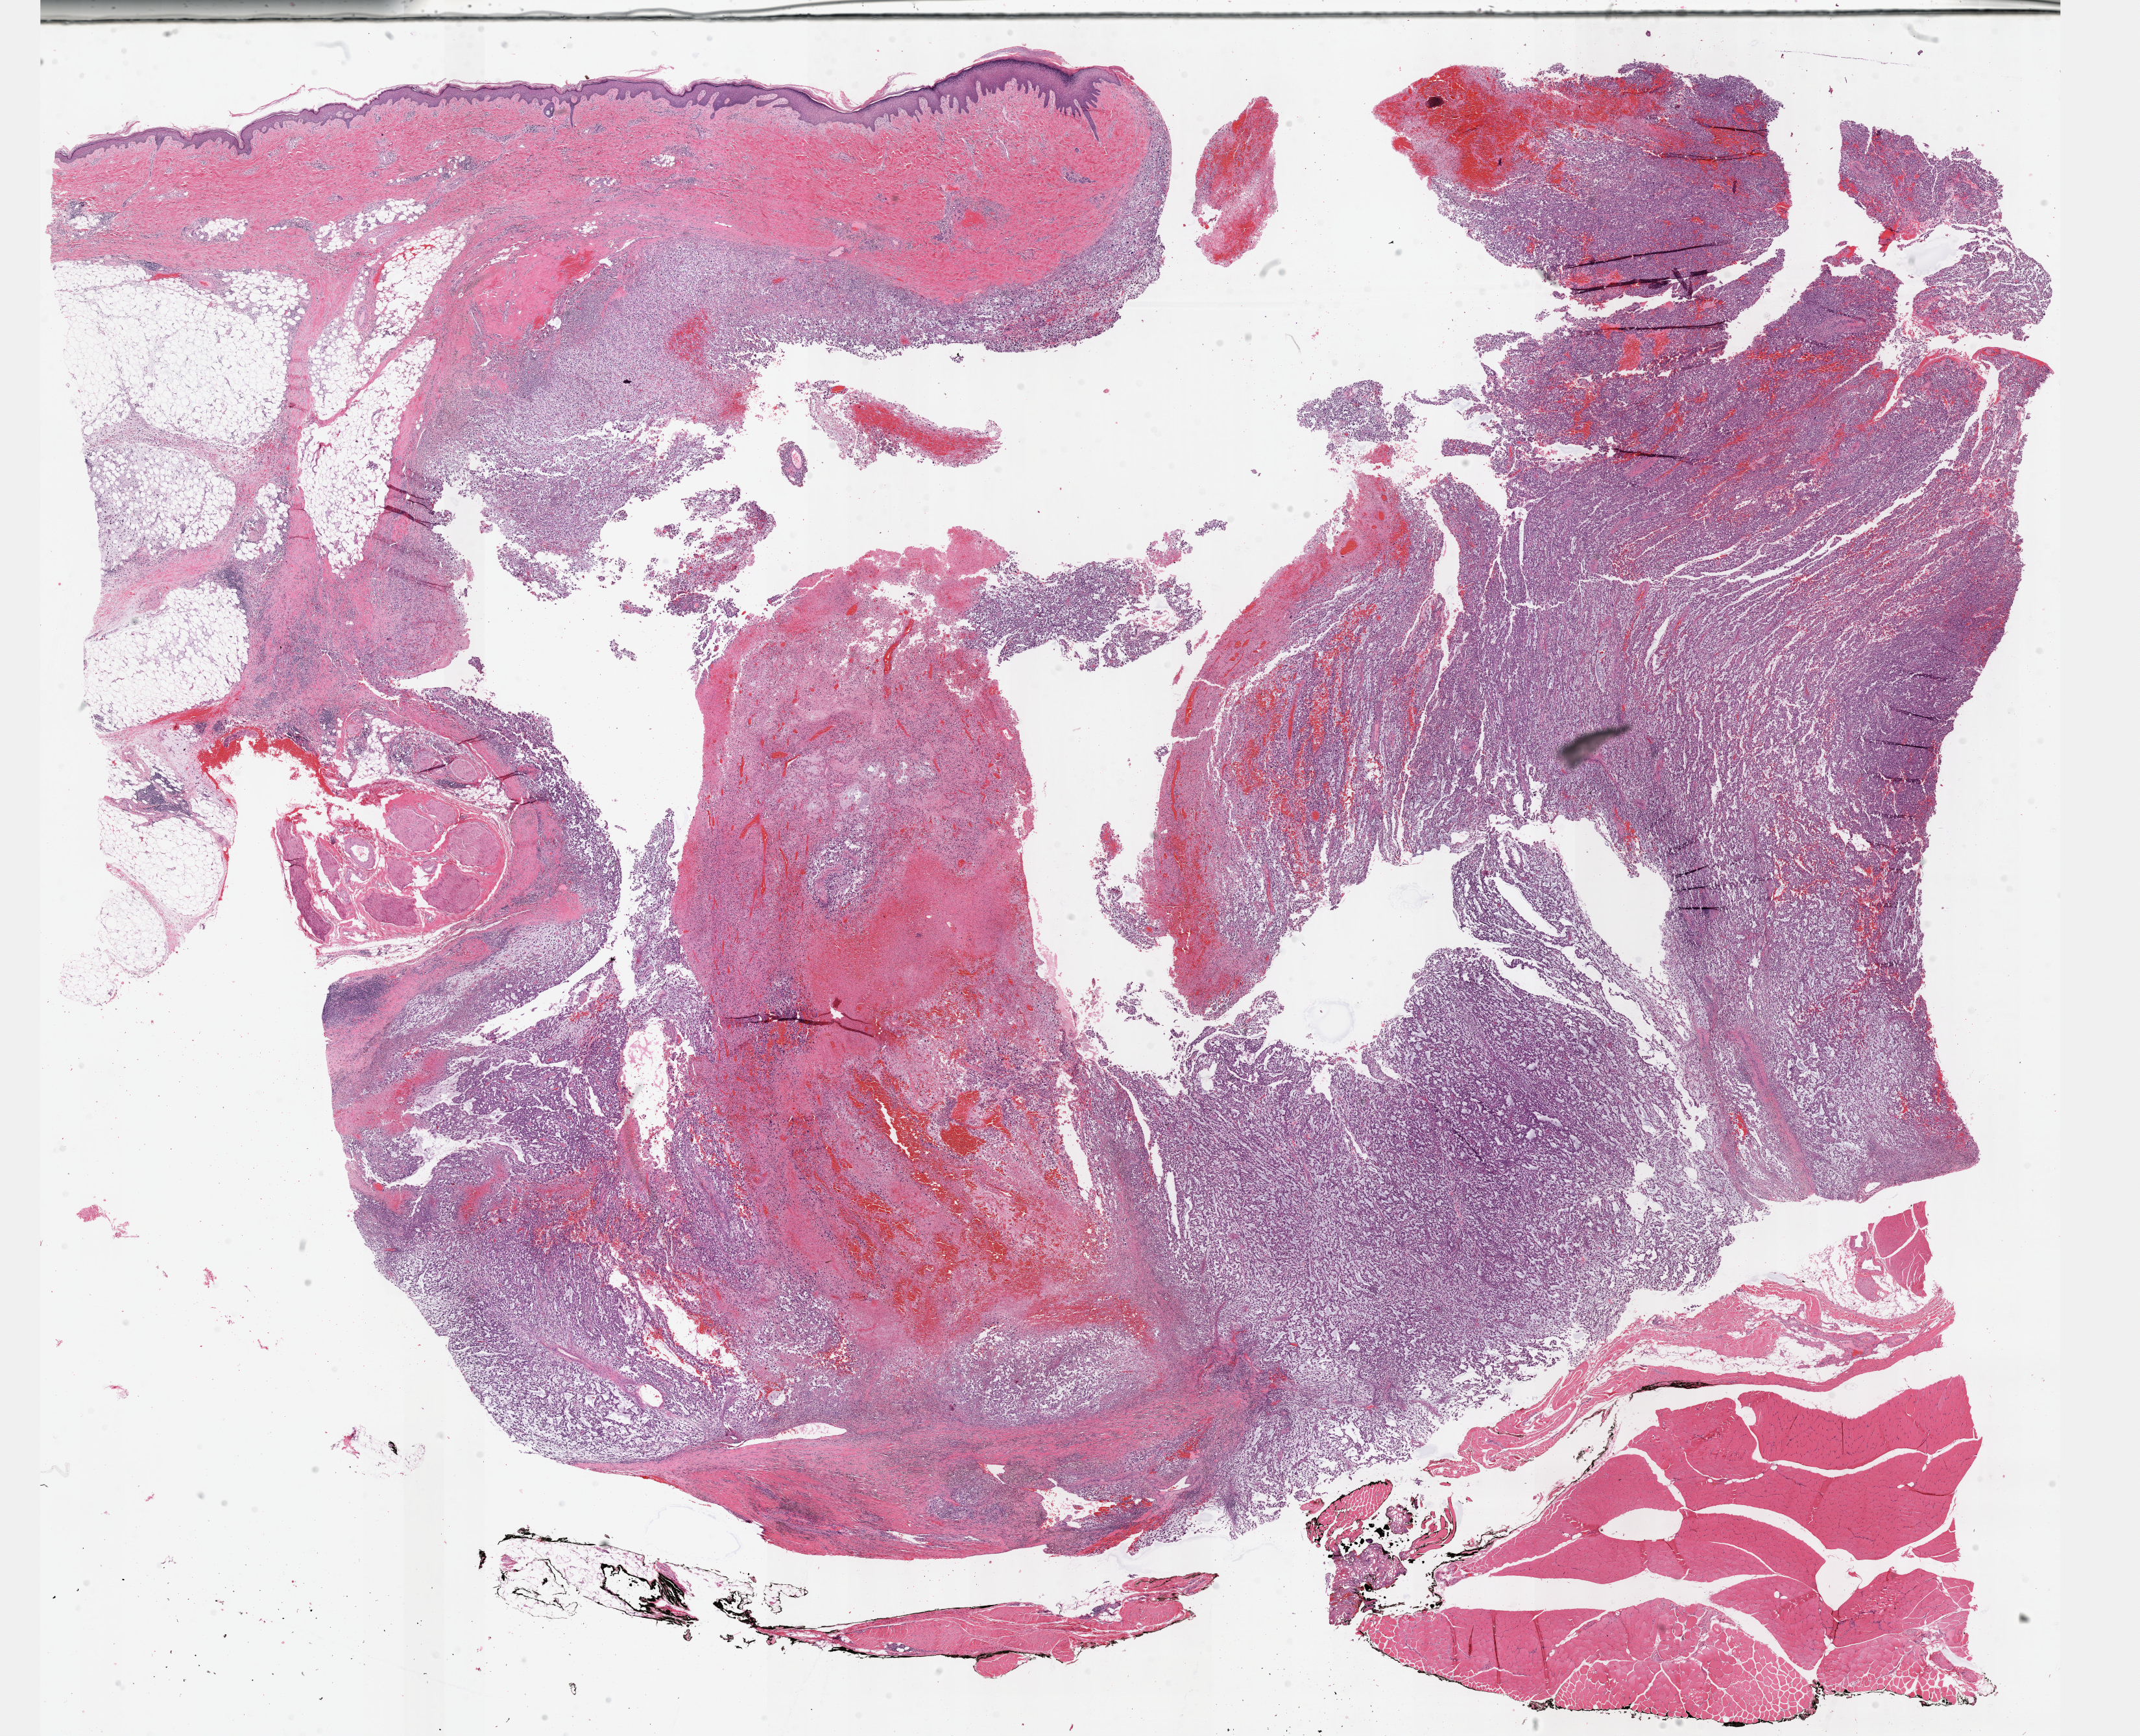
Whole-slide histology image, H&E, whole scanned area (about 26.7 x 21.6 mm) shown as a low-resolution overview, formalin-fixed paraffin-embedded (FFPE) diagnostic section, sample: primary tumour, connective, subcutaneous and other soft tissues. Patient: female, age at initial diagnosis 59 years.
Histologic diagnosis: Fibromyxosarcoma (connective, subcutaneous and other soft tissues of lower limb and hip).